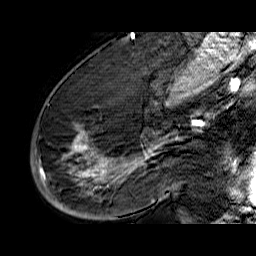
Breast MRI (dynamic contrast-enhanced), one sagittal slice. Position 37 of 60 along the scan axis. Dynamic contrast-enhanced series, time point 2 of 6 at this slice position (early post-contrast). 1.5 T. TE 6.5 ms, TR 32.9 ms. 4 mm slice thickness. 256 × 256 image matrix, field of view 200 × 200 mm. Female patient. From the clinical record (not read from this slice): setting: breast cancer imaged before/during neoadjuvant chemotherapy; receptor status: HR-positive, HER2-negative.
Outlined on this slice (semi-automatically segmented with operator editing):
- analysis volume of interest (the breast-tissue region the enhancement analysis was run in; not a lesion): bounding box (x1, y1, x2, y2) in pixels: (33, 74, 176, 210)
- tumour enhancement mask (voxels above the 100 % enhancement threshold inside the analysis volume of interest): (35, 133, 176, 192)